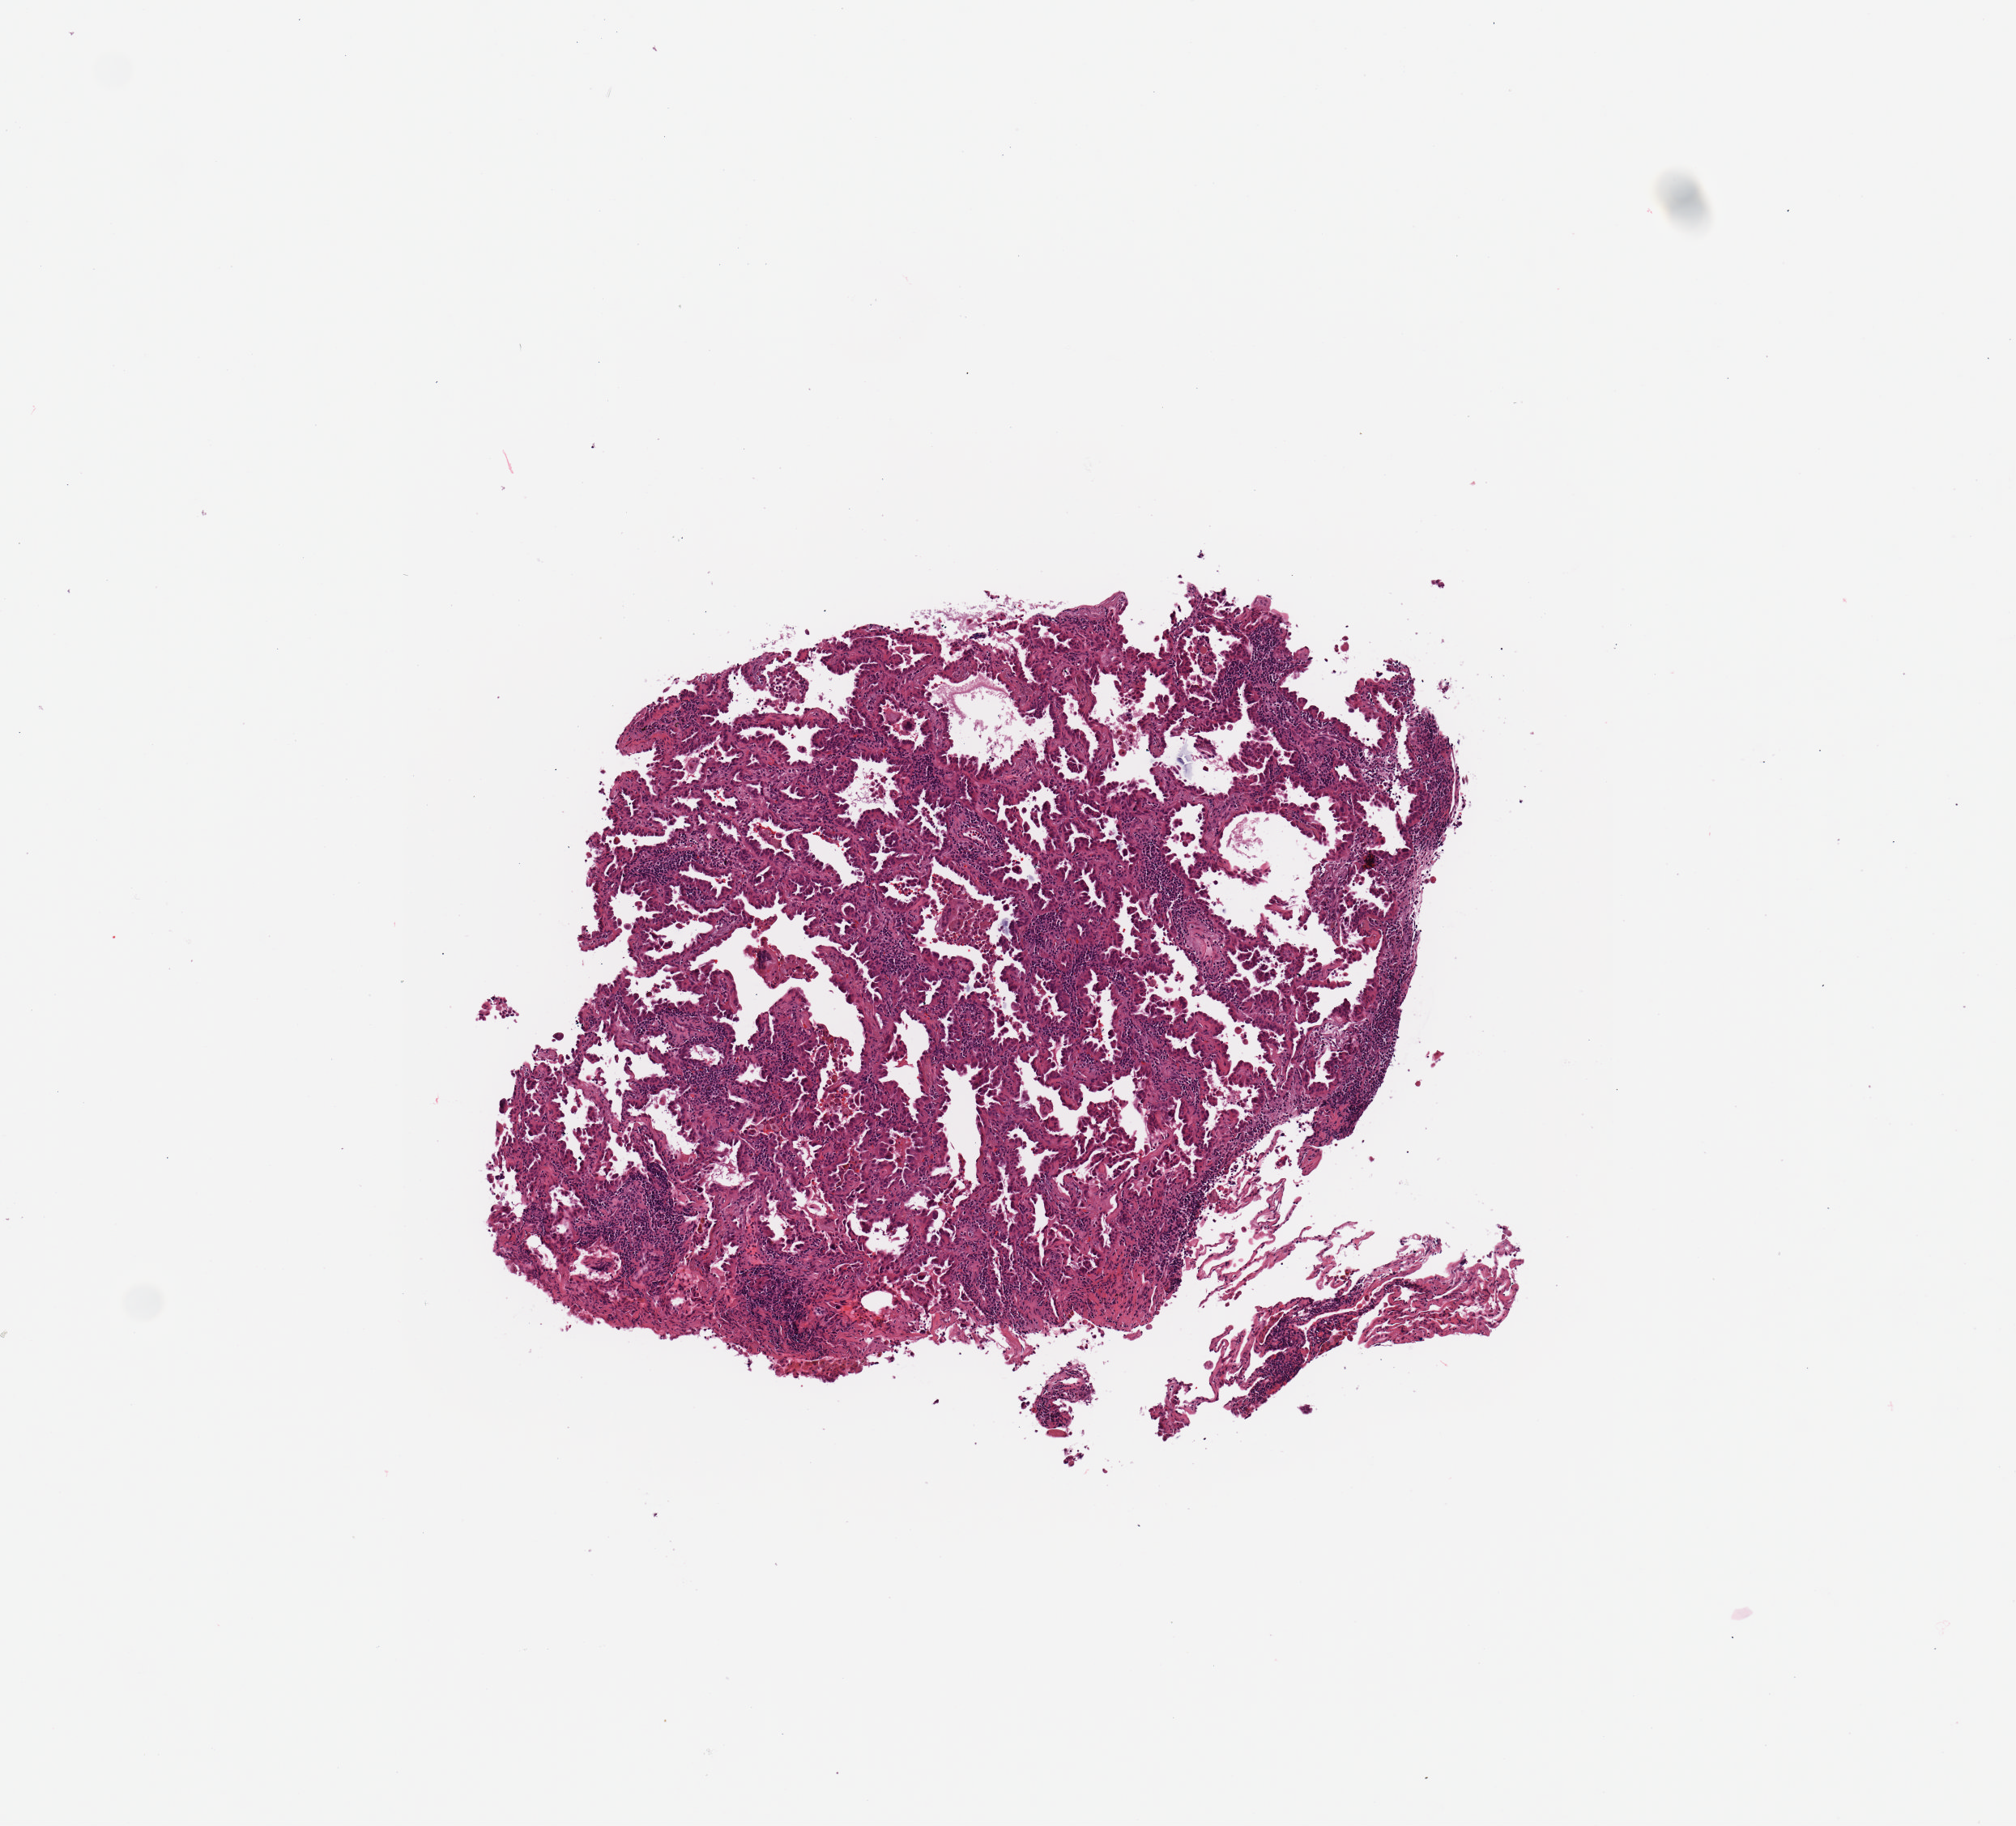
Whole-slide histology image, H&E-stained, shown as a low-resolution overview of the whole scanned area (about 4.9 x 4.5 mm); tumour tissue sample, lung. Female, 68 y/o. Histologic grade: G2 (moderately differentiated).
* AJCC pathologic stage: IB
* primary tumour site (as recorded): right upper lobe
* diagnosis: Adenocarcinoma, NOS